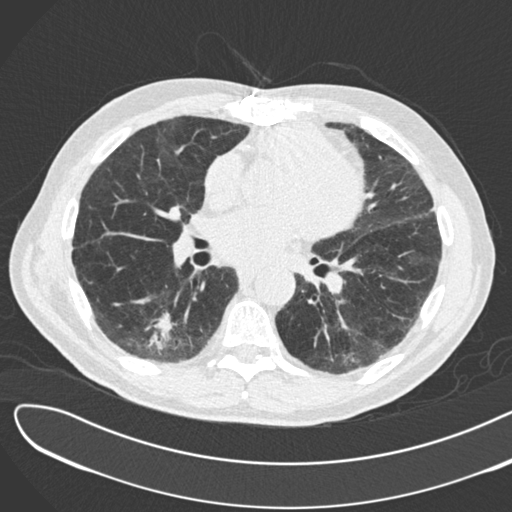
Low-dose screening chest CT, axial slice. Second annual screen. Lung window (W 1500 / L -600 HU). 2 mm slice thickness. Slice 101 of 183 in the series. 512 × 512 image matrix. Male participant, aged 72 years at enrolment.
- Expert reader's lesion annotation, bounding box (x1, y1, x2, y2) in pixels: (126, 289, 197, 355).
- The screening reader recorded 2 non-calcified nodules or masses ≥4 mm on this exam (right lower lobe, right lower lobe); which of them this box marks is not recorded.
- Lung cancer was diagnosed 46 days after this screen: squamous cell carcinoma, NOS, right lower lobe, poorly differentiated (G3), stage IB (AJCC 6th edition), 42 mm at pathology.